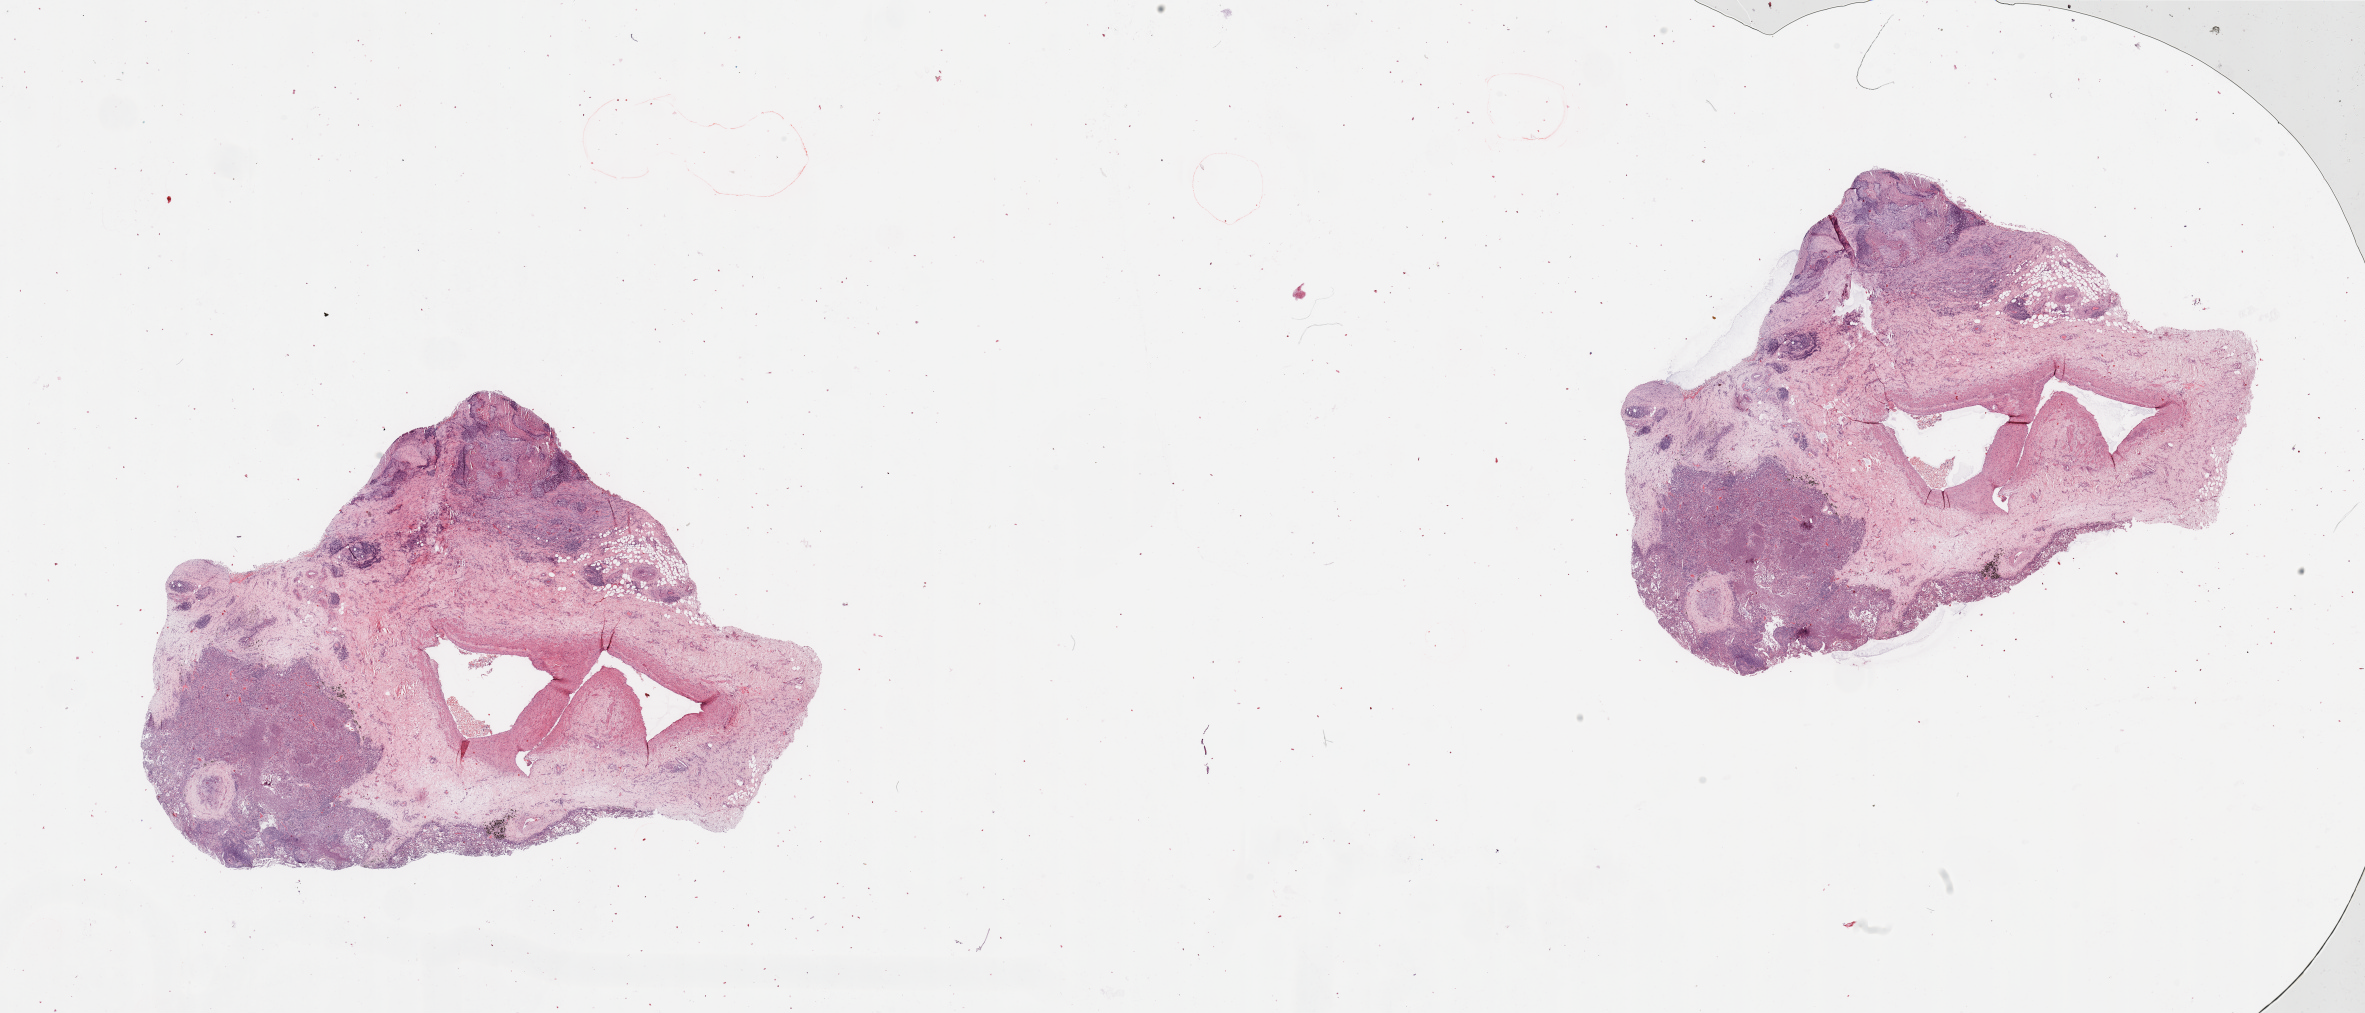
H&E whole-slide image, shown as a low-resolution overview of the whole scanned area (about 37.4 x 16.0 mm, from a 20x scan); tumour tissue sample, lung. Patient: male, age 65 years. Histologic grade: G3 (poorly differentiated).
- AJCC pathologic stage: IB
- diagnosis: Squamous cell carcinoma, NOS